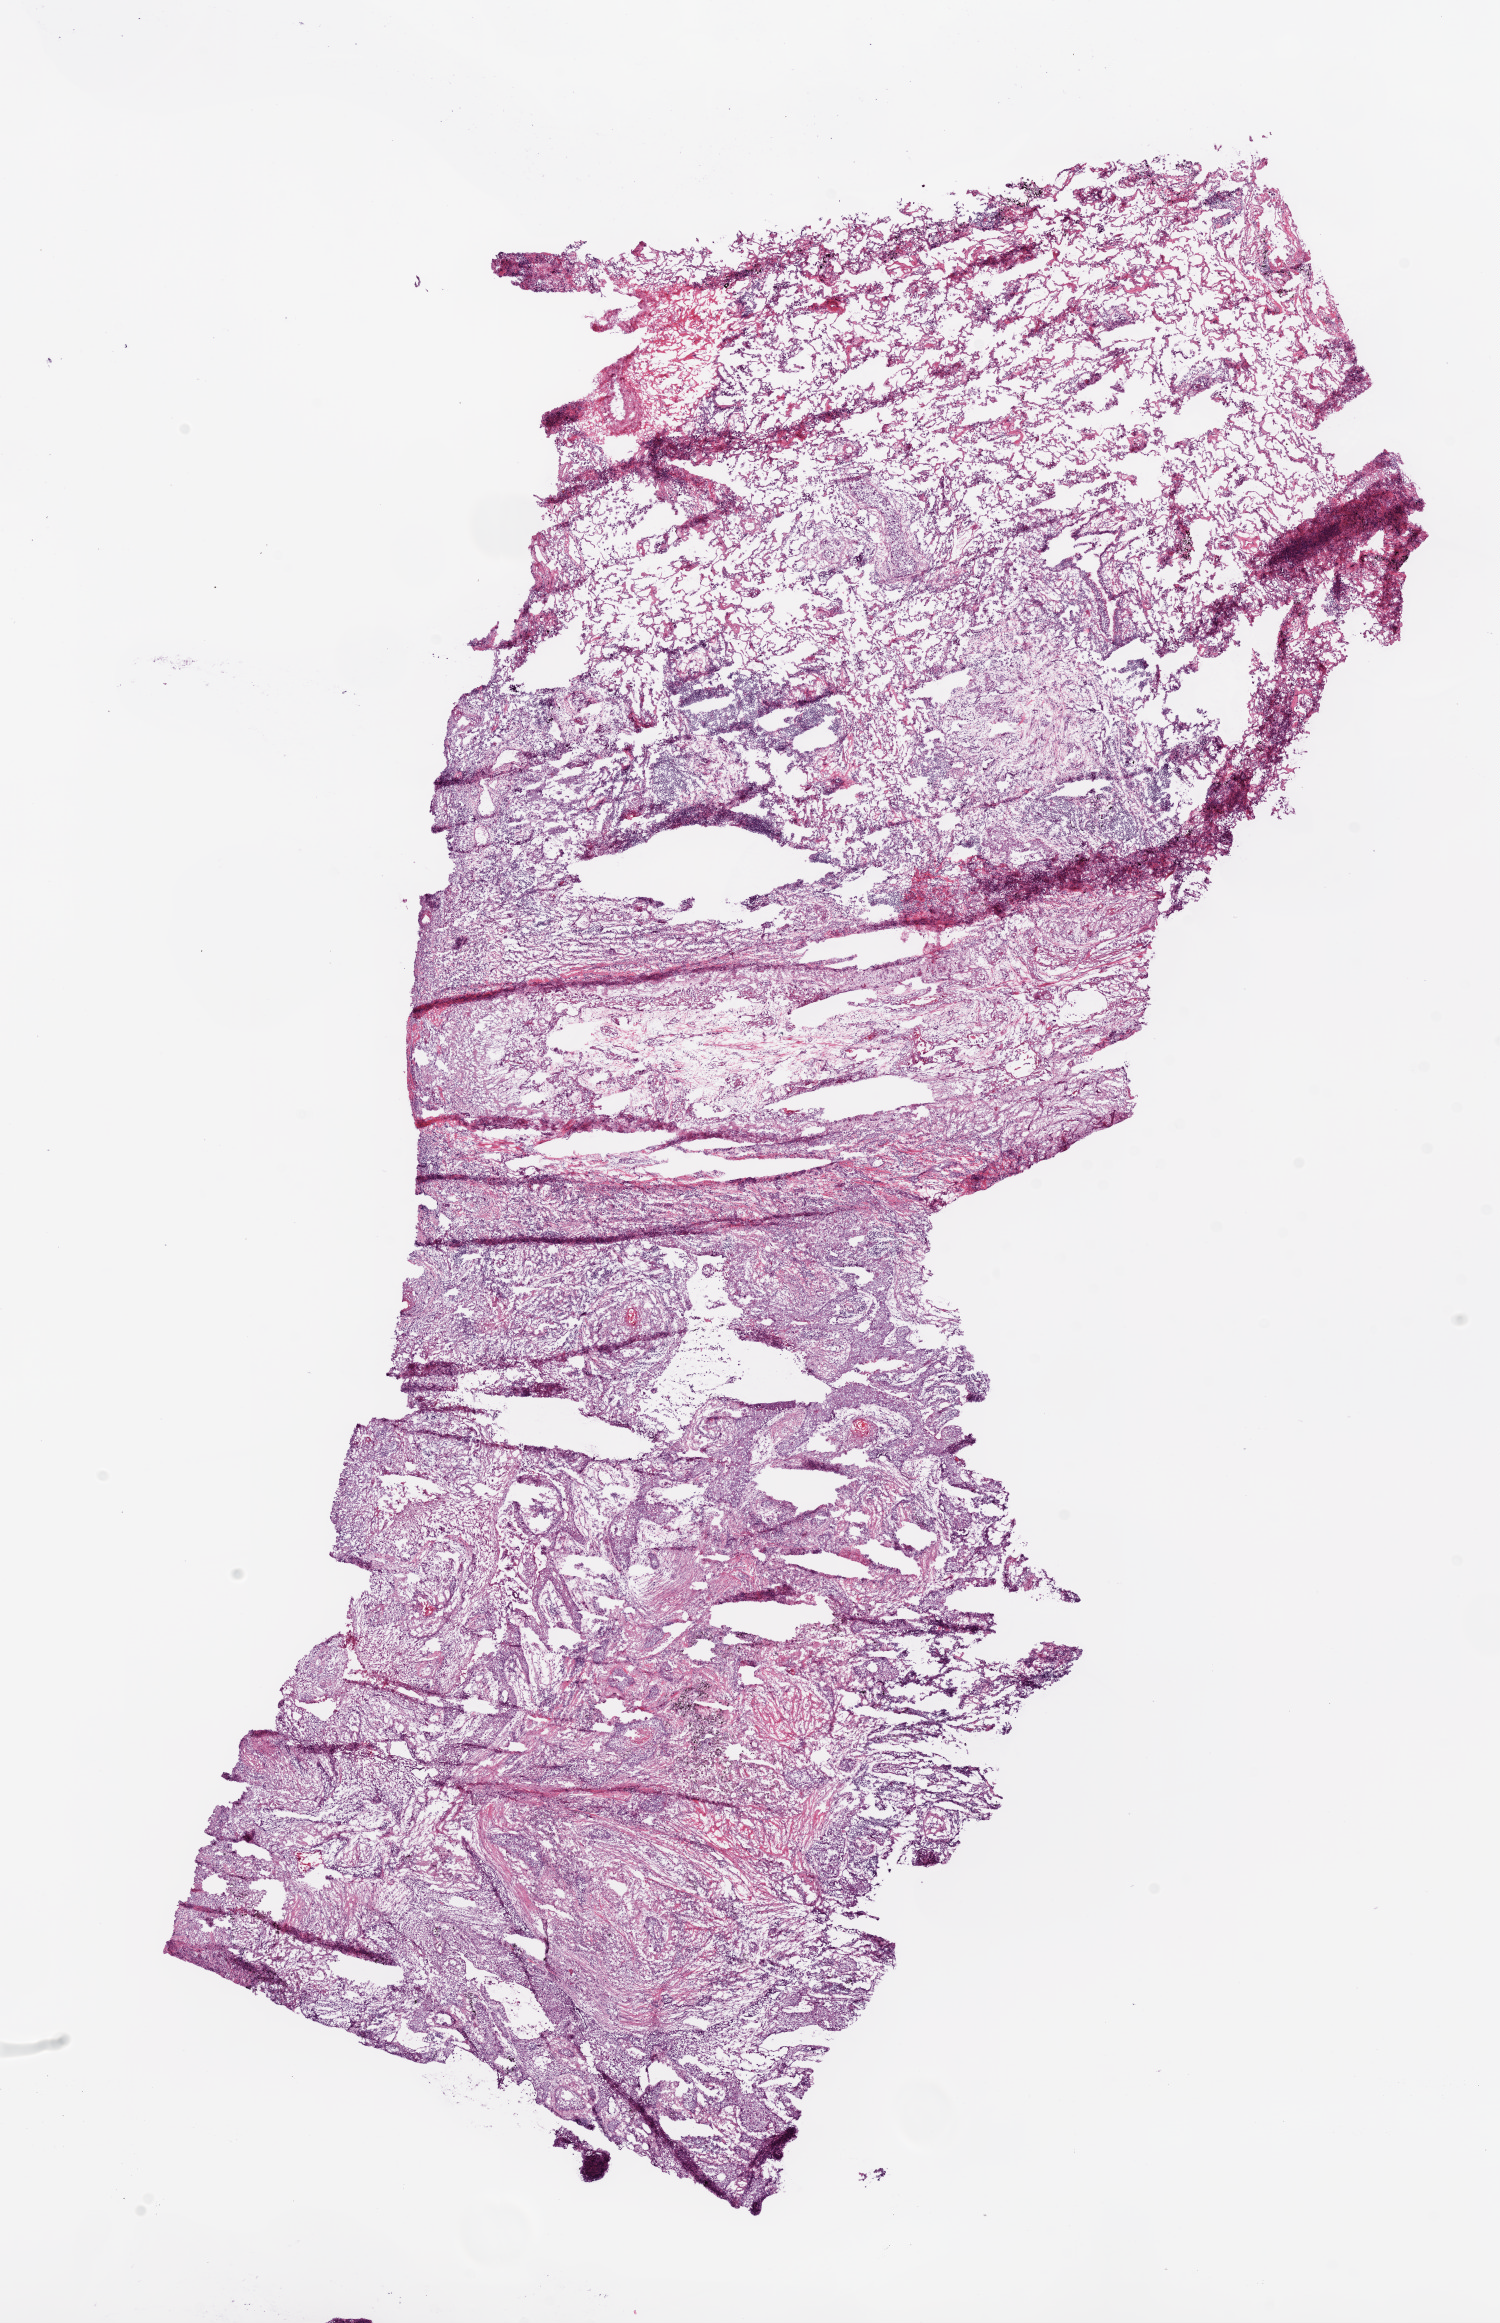
Digitized H&E-stained tissue section (whole slide) — a low-resolution overview of the entire scanned area, about 12.0 x 18.6 mm (from a 20x scan), frozen section, primary tumour sample from the lung. Patient: male, age at initial diagnosis 84 years. Slide review estimates, as recorded: tumour cells 78%, tumour nuclei 80%, normal cells 10%, stromal cells 10%, necrosis 2%. Inflammatory infiltration, as recorded: lymphocyte infiltration 5%, monocyte infiltration 2%.
Diagnosis: Squamous cell carcinoma, NOS (upper lobe, lung). AJCC pathologic stage: IB. Laterality: left.